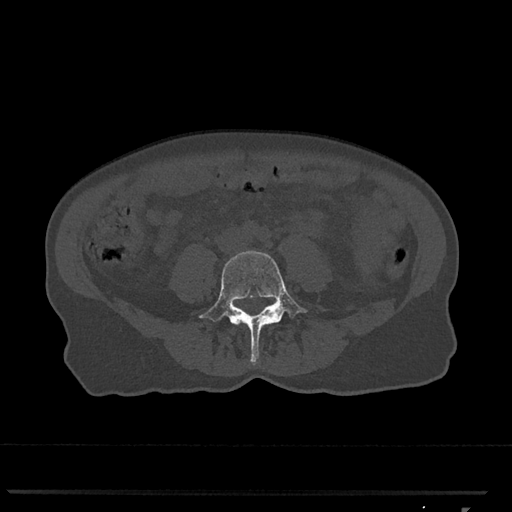
CT including the spine, one axial slice; position 212 of 793 along the scan axis; reconstruction kernel Br40s/3; bone window (W 1800 / L 400 HU); 0.5 mm slice thickness; 512 × 512 image matrix. Female patient, age 62 years. From the clinical record (not read from this slice): primary cancer: renal.
Structures marked on this image (semi-automatic segmentation, software-assisted and operator-edited):
- L4 vertebra: bounding box (x1, y1, x2, y2) in pixels: (198, 250, 307, 364)